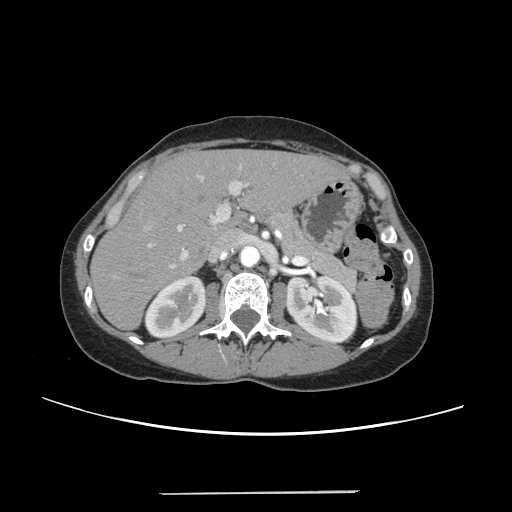
Contrast-enhanced abdominal CT, one axial slice; position 146 of 240 along the scan axis; 120 kVp; intravenous contrast given; soft-tissue window (W 400 / L 40 HU); 512 × 512 image matrix. Female patient, age 60 years. From the clinical record (not read from this slice): diagnosis: colorectal cancer liver metastases, imaged before liver resection; multiple liver metastases: no; largest metastasis: 1.5 cm; disease in both lobes: no.
Structures marked on this image (expert manual segmentation):
- liver: box from (x=93, y=151) to (x=344, y=328) px
- planned liver remnant (the part of the liver to remain after resection): (x=93, y=150)–(x=343, y=328)
- portal vein (with intrahepatic branches): (x=144, y=164)–(x=249, y=268)